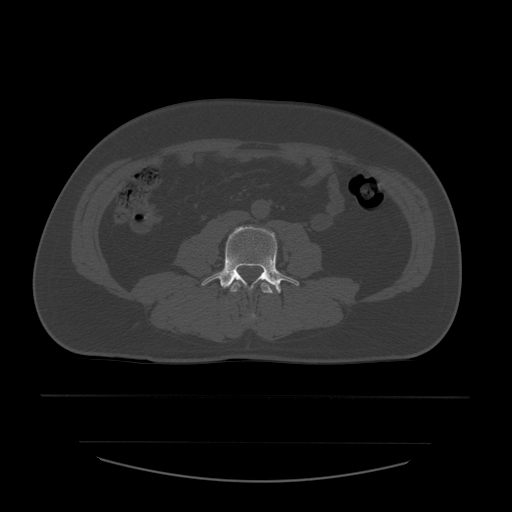
CT including the spine, one axial slice; slice 153 of 532 in the series (ordered by position); 120 kVp; bone window (W 1800 / L 400 HU); 1.25 mm slice thickness; 512 × 512 image matrix, field of view 441 × 441 mm. Patient age 44 years. Case-level facts recorded for this patient, not image findings: primary cancer: soft tissue sarcoma.
Structures marked on this image (semi-automatic segmentation, software-assisted and operator-edited):
- L3 vertebra: bounding box [x1, y1, x2, y2] px = [231, 282, 274, 318]
- L4 vertebra: [201, 226, 300, 294]